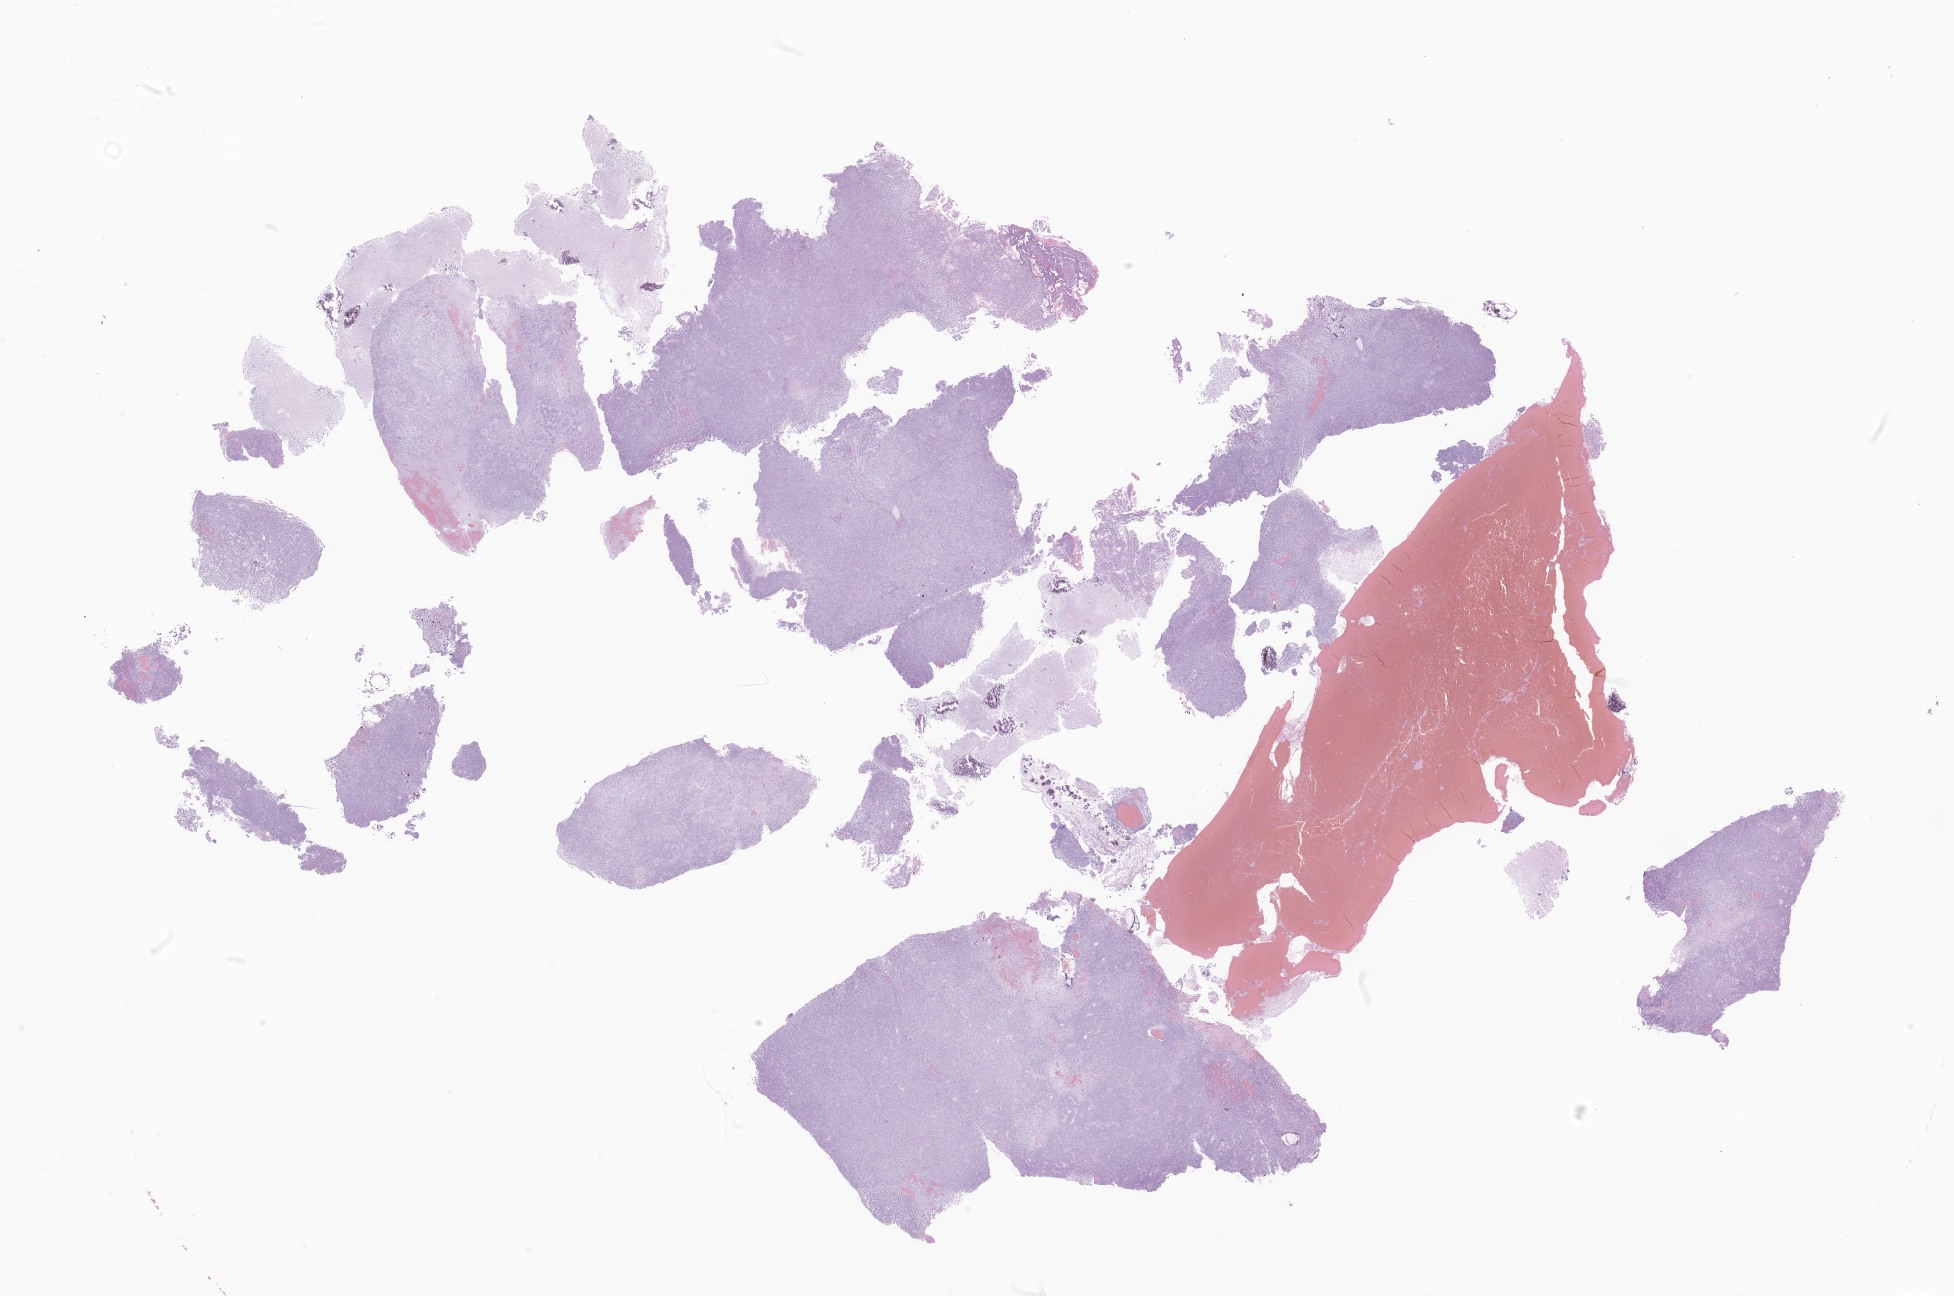
Whole-slide image, hematoxylin and eosin (H&E) stain of tumor tissue from the brain — a low-resolution overview of the entire scanned area, about 33.0 x 21.9 mm; formalin-fixed, paraffin-embedded (FFPE) tissue. Male patient, age 59 months (4 years 11 months).
- diagnosis (ICD-O-3 morphology term): Neoplasm, uncertain whether benign or malignant